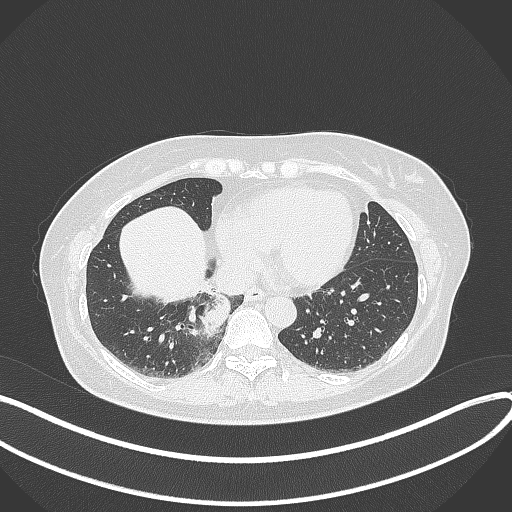
Chest CT, one axial slice. Slice 108 of 331 in the series (ordered by position). Reconstruction kernel B70f. 120 kVp. Lung window (W 1500 / L -600 HU). 1 mm slice thickness. 512 × 512 image matrix. Female patient, age 54 years. Case-level facts recorded for this patient, not image findings: clinical TNM (as recorded): T4 N0 M0.
Annotated regions visible in this slice (rectangle marked by the reading radiologist):
- lung tumour (recorded histology: adenocarcinoma): bounding box (x1, y1, x2, y2) in pixels: (200, 289, 232, 337)